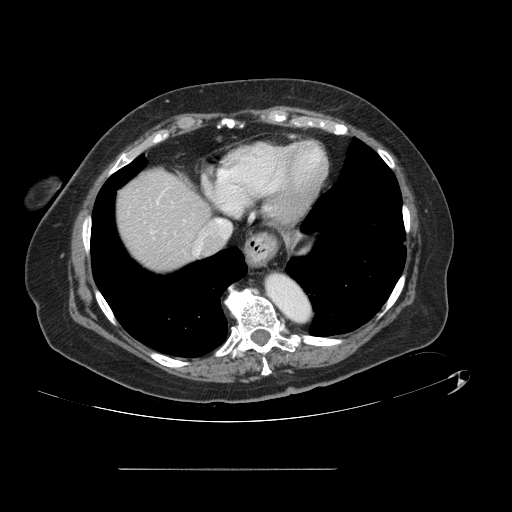
Contrast-enhanced abdominal CT, one axial slice. Slice 121 of 148 in the series (ordered by position). Intravenous contrast given. Soft-tissue window (W 400 / L 40 HU). 2.5 mm slice thickness. 512 × 512 image matrix, field of view 439 × 439 mm. Female patient, age 75 years. Case-level facts recorded for this patient, not image findings: diagnosis: colorectal cancer liver metastases, imaged before liver resection; multiple liver metastases: no; largest metastasis: 2.4 cm.
Structures marked on this image (expert manual segmentation):
- hepatic veins: box from (x=196, y=219) to (x=231, y=254) px
- liver: (x=118, y=171)–(x=208, y=272)
- planned liver remnant (the part of the liver to remain after resection): (x=117, y=170)–(x=208, y=272)